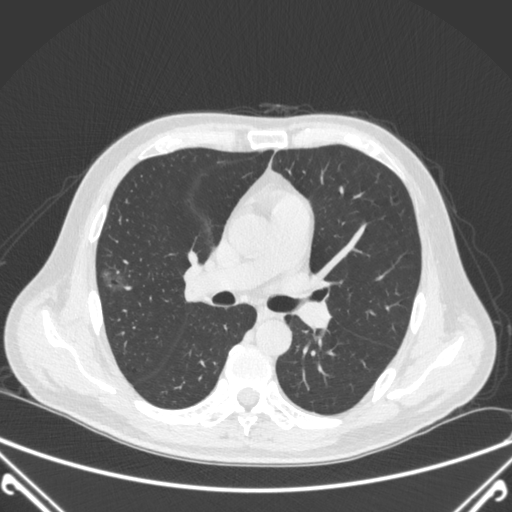
Chest CT, one axial slice. Position 219 of 360 along the scan axis. 120 kVp. Lung window (W 1500 / L -600 HU). 1 mm slice thickness. 512 × 512 image matrix, field of view 380 × 380 mm. Patient: male, 64 years. From the clinical record (not read from this slice): clinical TNM (as recorded): T1c N0 M0.
Outlined on this slice (rectangle marked by the reading radiologist):
- lung tumour (recorded histology: adenocarcinoma): bounding box <99,259,144,307> (left, top, right, bottom; pixels)